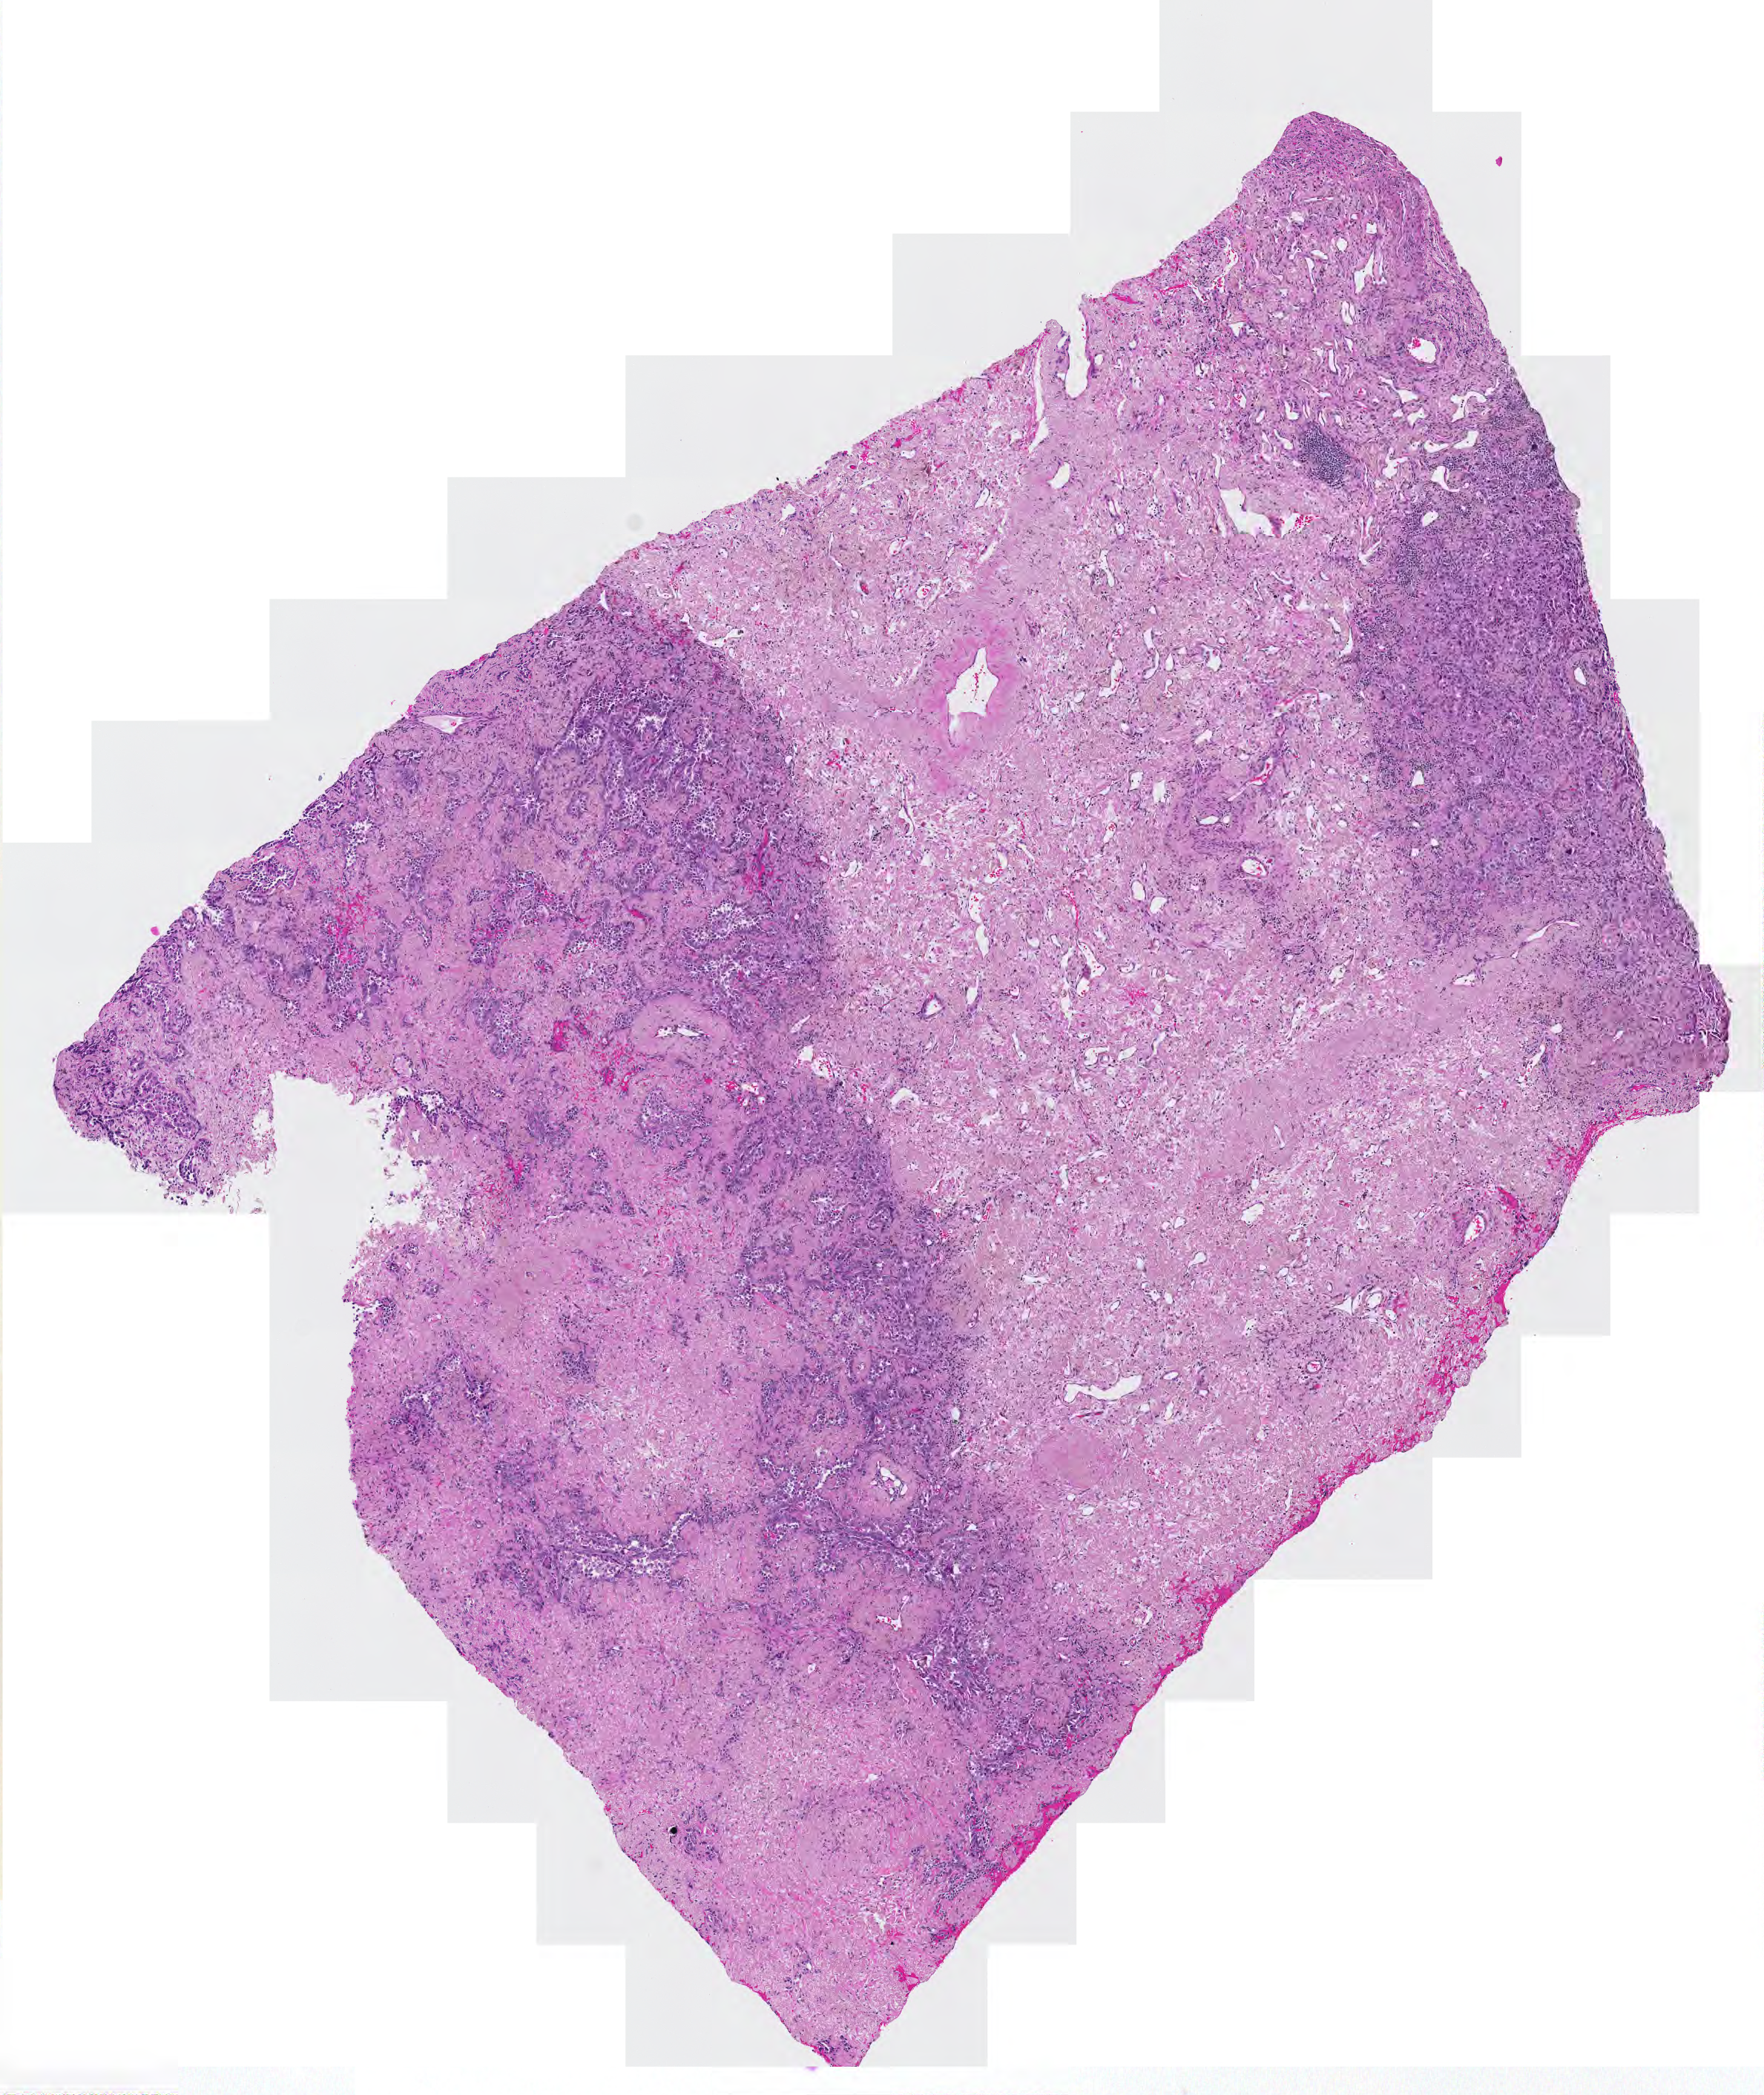
Hematoxylin and eosin (H&E) stained whole-slide image, a low-resolution overview of the entire scanned area, about 6.1 x 7.3 mm, lung, tumour tissue. Patient: female, age 68 years. Histologic grade: G2 (moderately differentiated).
* primary tumour site (as recorded): right upper lobe
* histologic diagnosis: Adenocarcinoma, NOS
* AJCC pathologic stage: IA